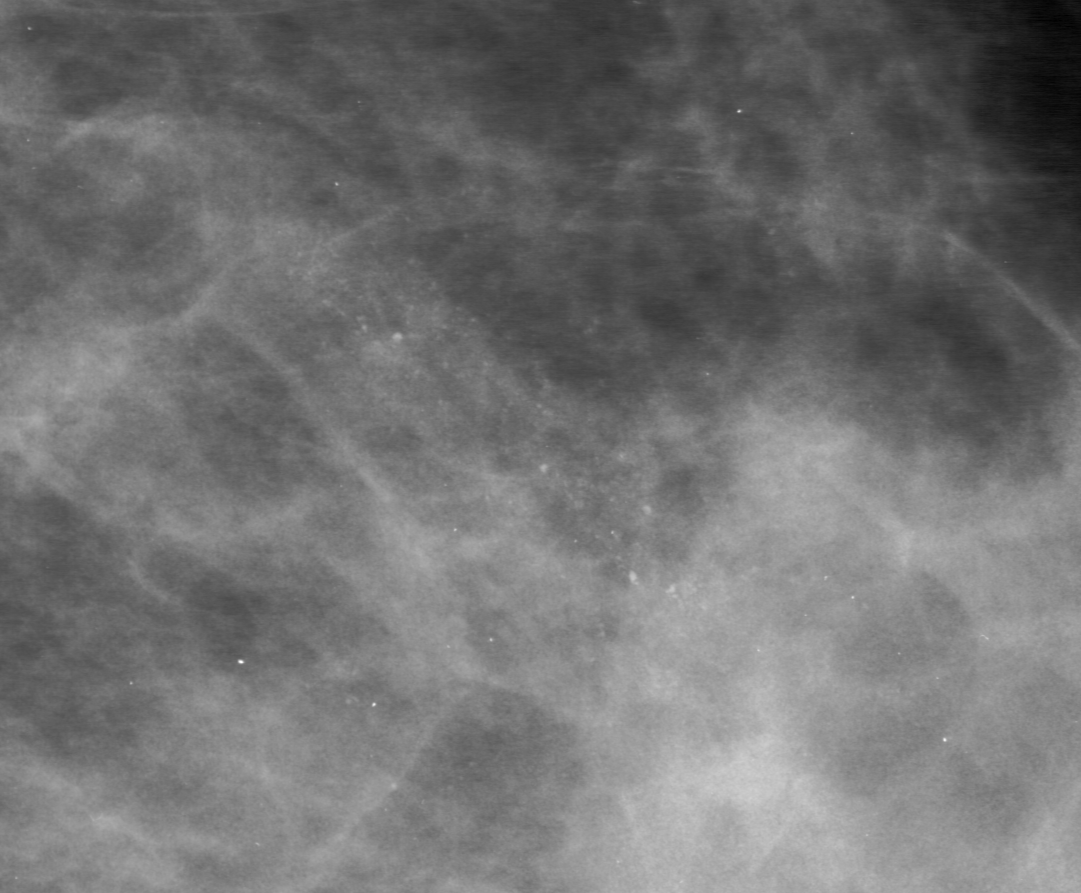
Cropped region of a digitized screen-film mammogram centred on a radiologist-marked abnormality; left breast; MLO view; BI-RADS breast density category 3 (scale 1–4).
Calcifications, morphology amorphous, distribution segmental; BI-RADS assessment category 0 (incomplete: needs additional imaging); subtlety rating 4 on a 1 (subtle) to 5 (obvious) scale; pathology result (as recorded, not read from the image): benign.